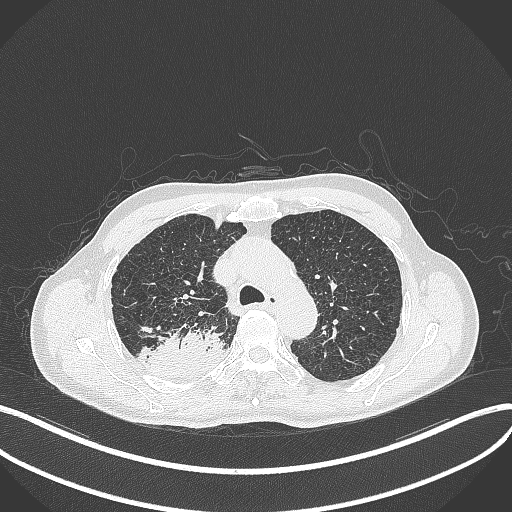
Chest CT, one axial slice. Position 326 of 428 along the scan axis. Lung window (W 1500 / L -600 HU). 512 × 512 image matrix, field of view 400 × 400 mm. Male patient, age 79 years. Case-level facts recorded for this patient, not image findings: clinical TNM (as recorded): T3 N0 M0.
Annotated regions visible in this slice (rectangle marked by the reading radiologist):
- lung tumour (recorded histology: adenocarcinoma): bounding box (x1, y1, x2, y2) in pixels: (137, 324, 226, 381)